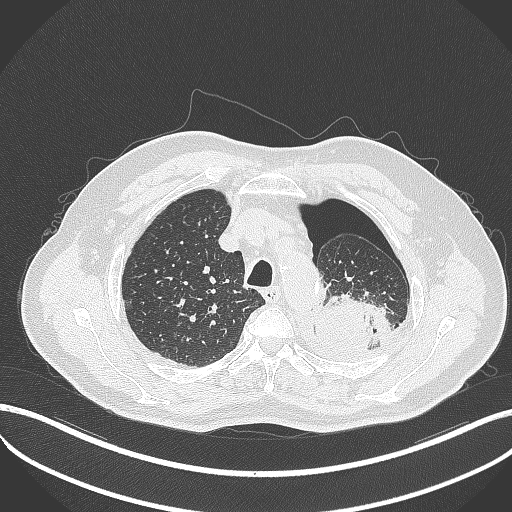
Chest CT, one axial slice; position 401 of 464 along the scan axis; reconstruction kernel B70f; 120 kVp; lung window (W 1500 / L -600 HU); 1 mm slice thickness; 512 × 512 image matrix, field of view 400 × 400 mm. Patient: male, 76 years. From the clinical record (not read from this slice): clinical TNM (as recorded): T3 N0 M1b.
Annotated regions visible in this slice (rectangle marked by the reading radiologist):
- lung tumour (recorded histology: adenocarcinoma): bounding box [x1, y1, x2, y2] px = [312, 291, 392, 357]